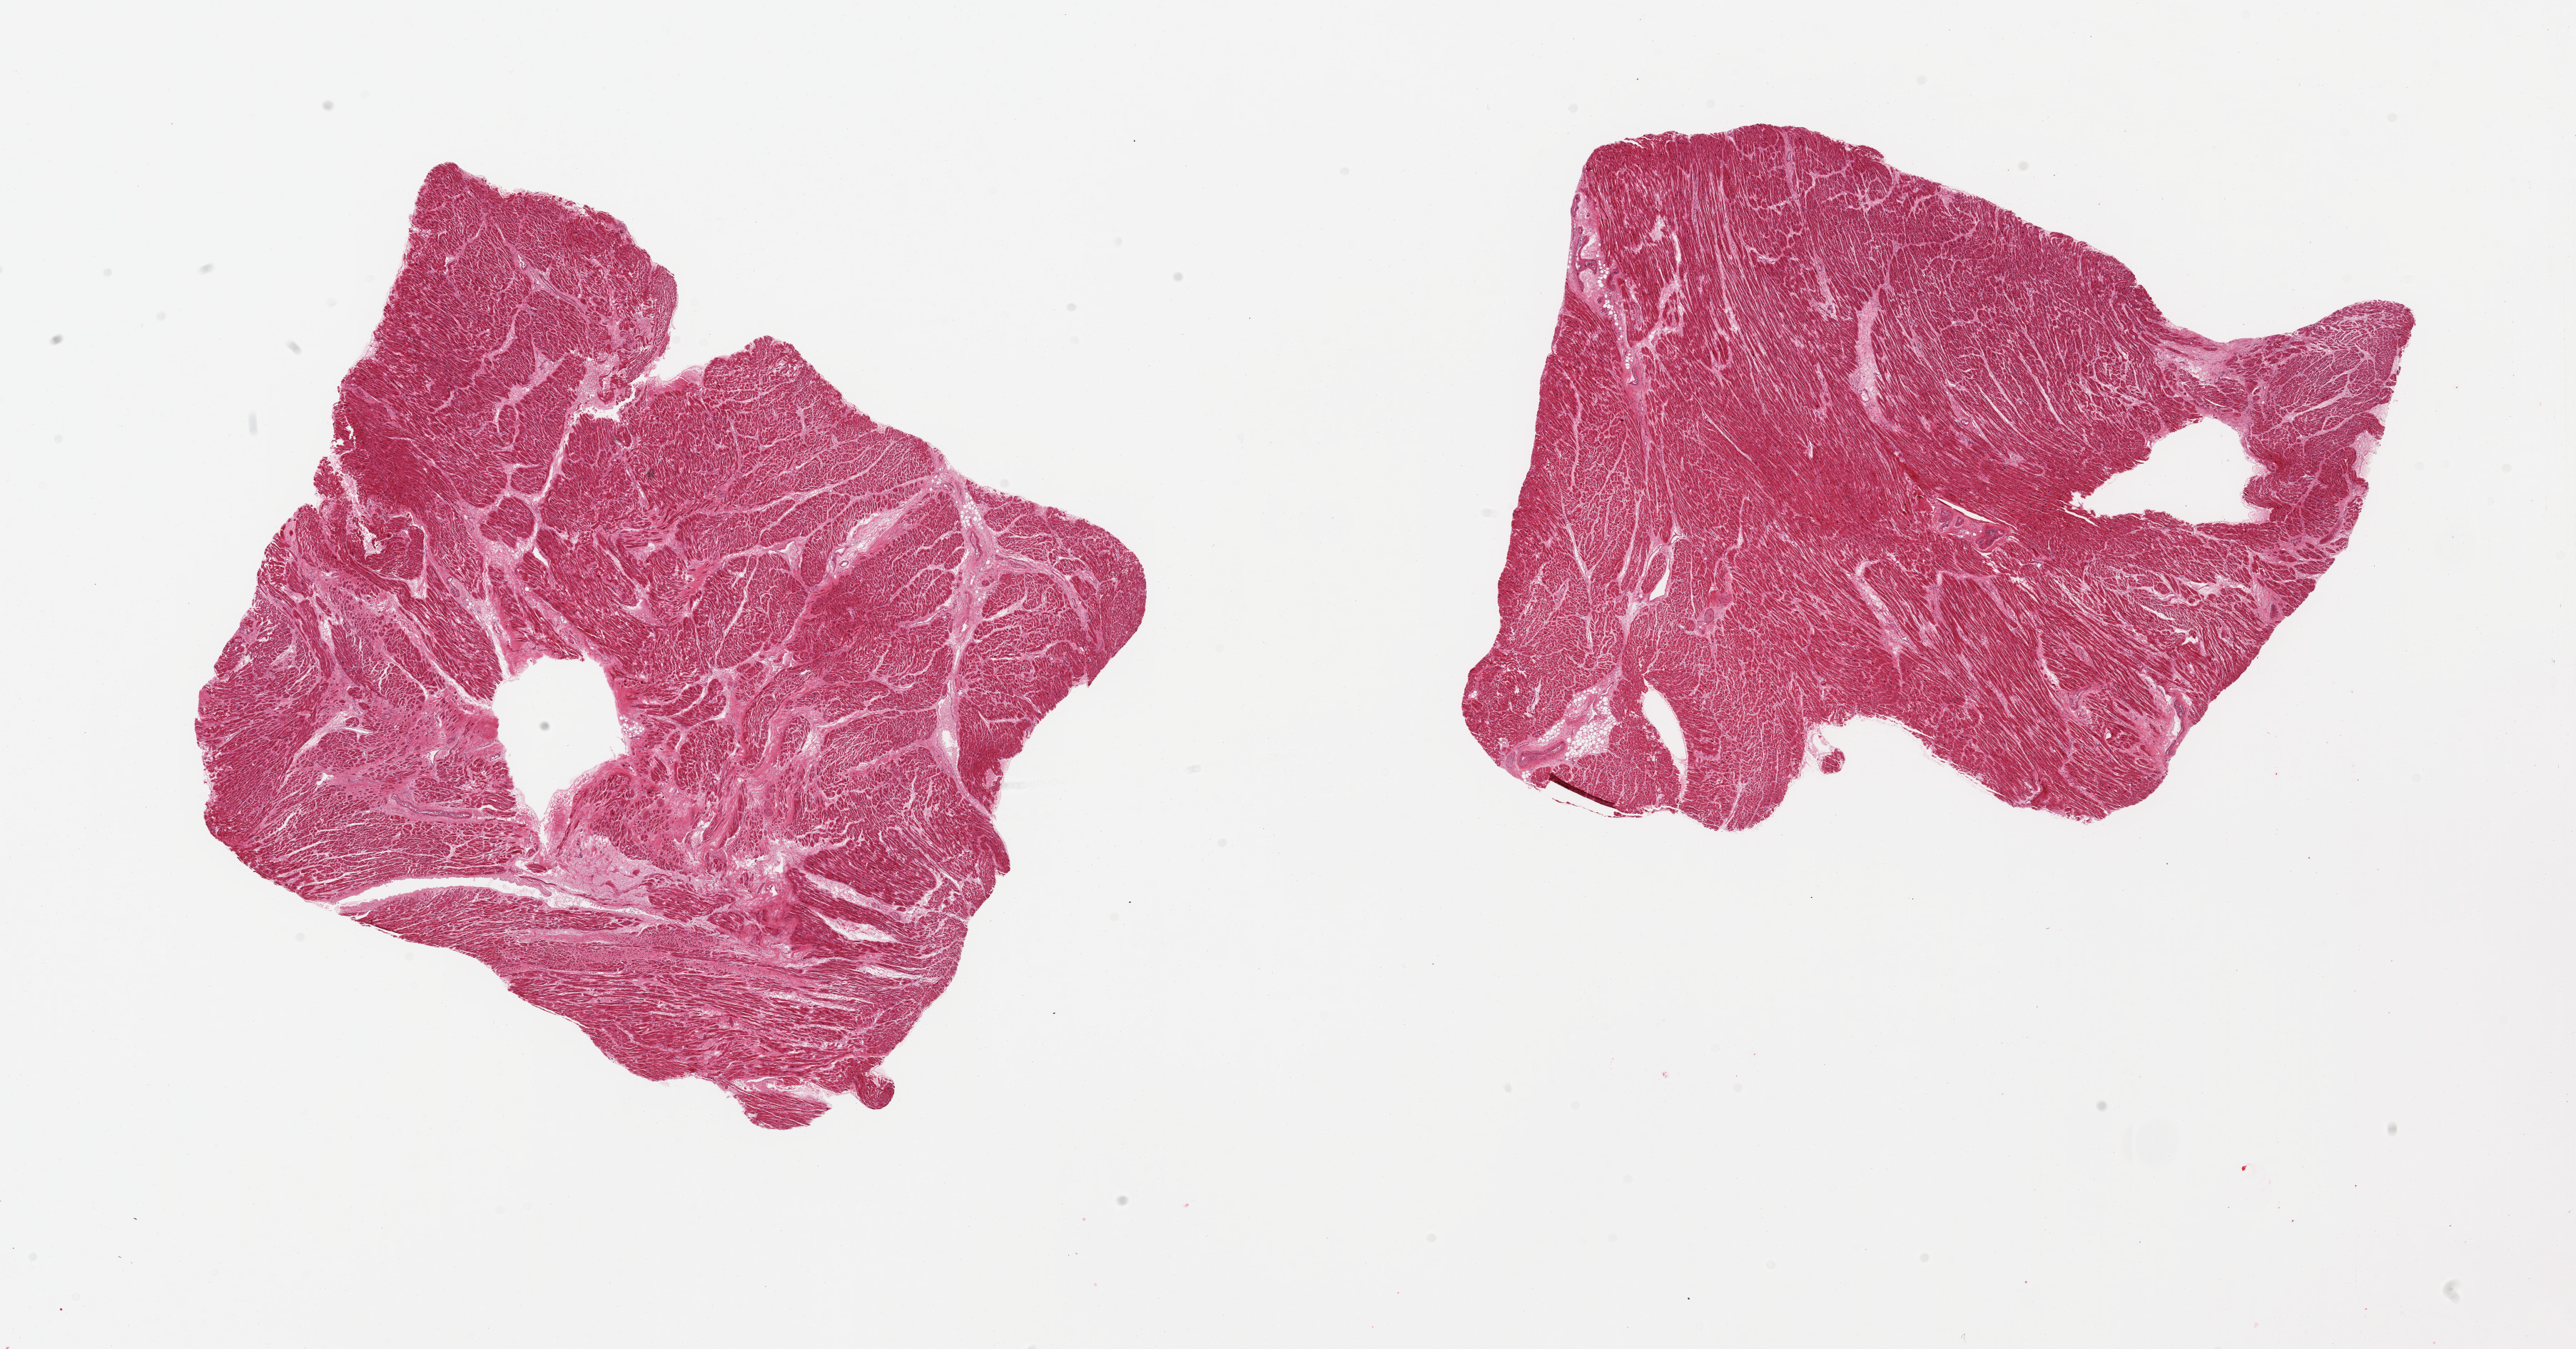
Hematoxylin and eosin (H&E) whole-slide image, brightfield — low-resolution overview of the scanned area, about 28.5 x 14.9 mm (from a 20x scan). PAXgene-fixed paraffin-embedded (PFPE) section. Sampled site (target tissue): heart. Tissue donor sample.
Pathologist's review note for this sample: 2 pieces, micro infarcts, moderate-marked chronic ischemic damage.